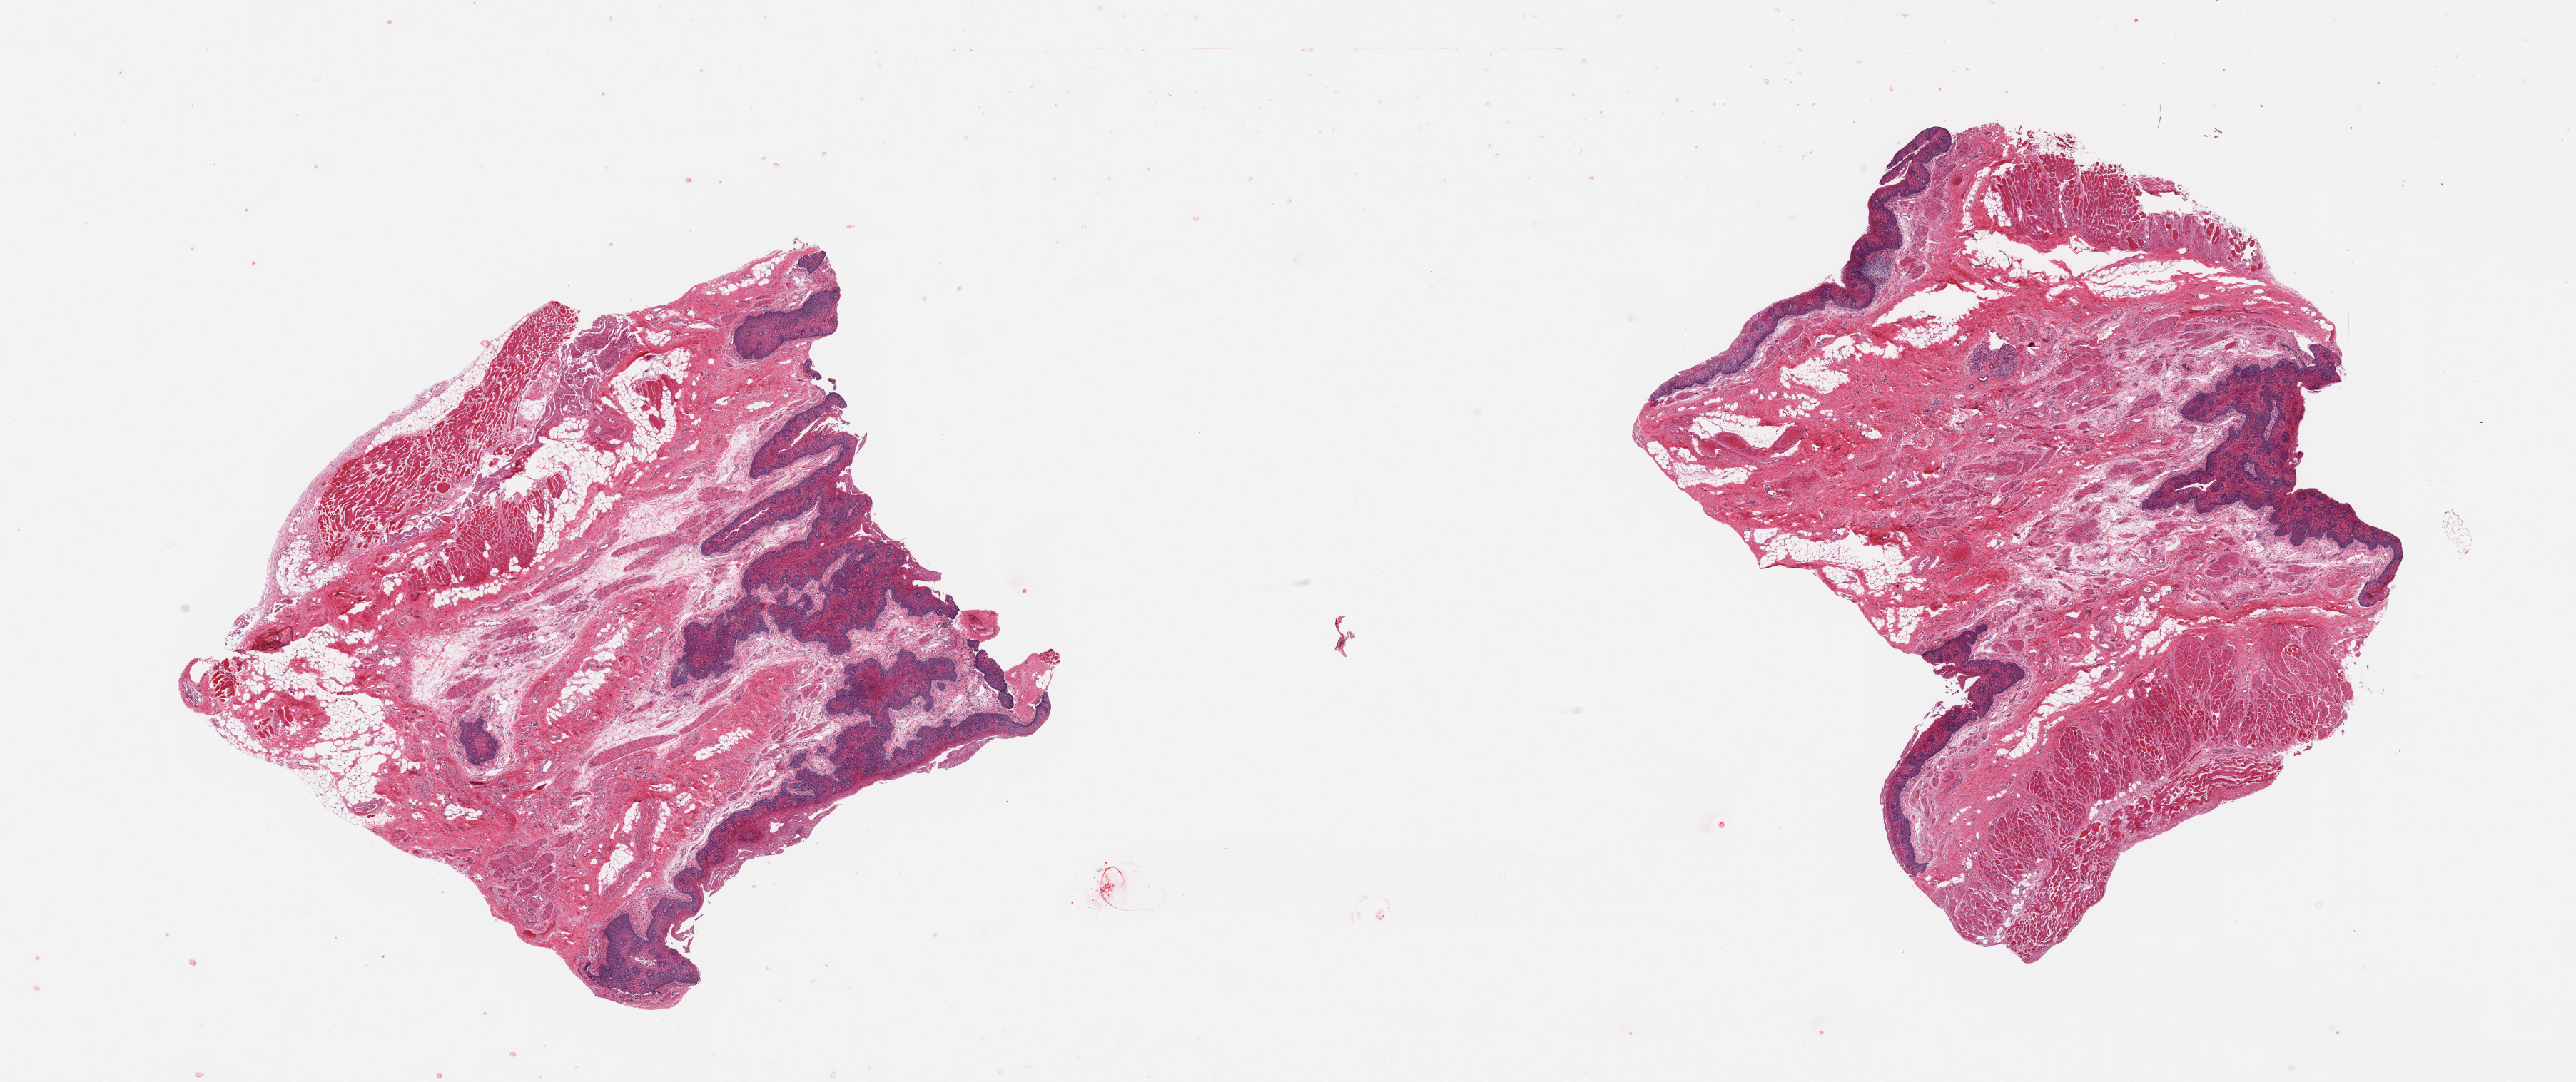
Digitized haematoxylin and eosin-stained section, low-resolution overview of the scanned area, about 28.5 x 12.0 mm, PAXgene-fixed paraffin-embedded (PFPE) section, target tissue: thyroid, donor tissue sample.
Review note (as recorded): 2 pieces; squamous epithelium, nerve, skeletal muscle, soft tissue, not thyroid.